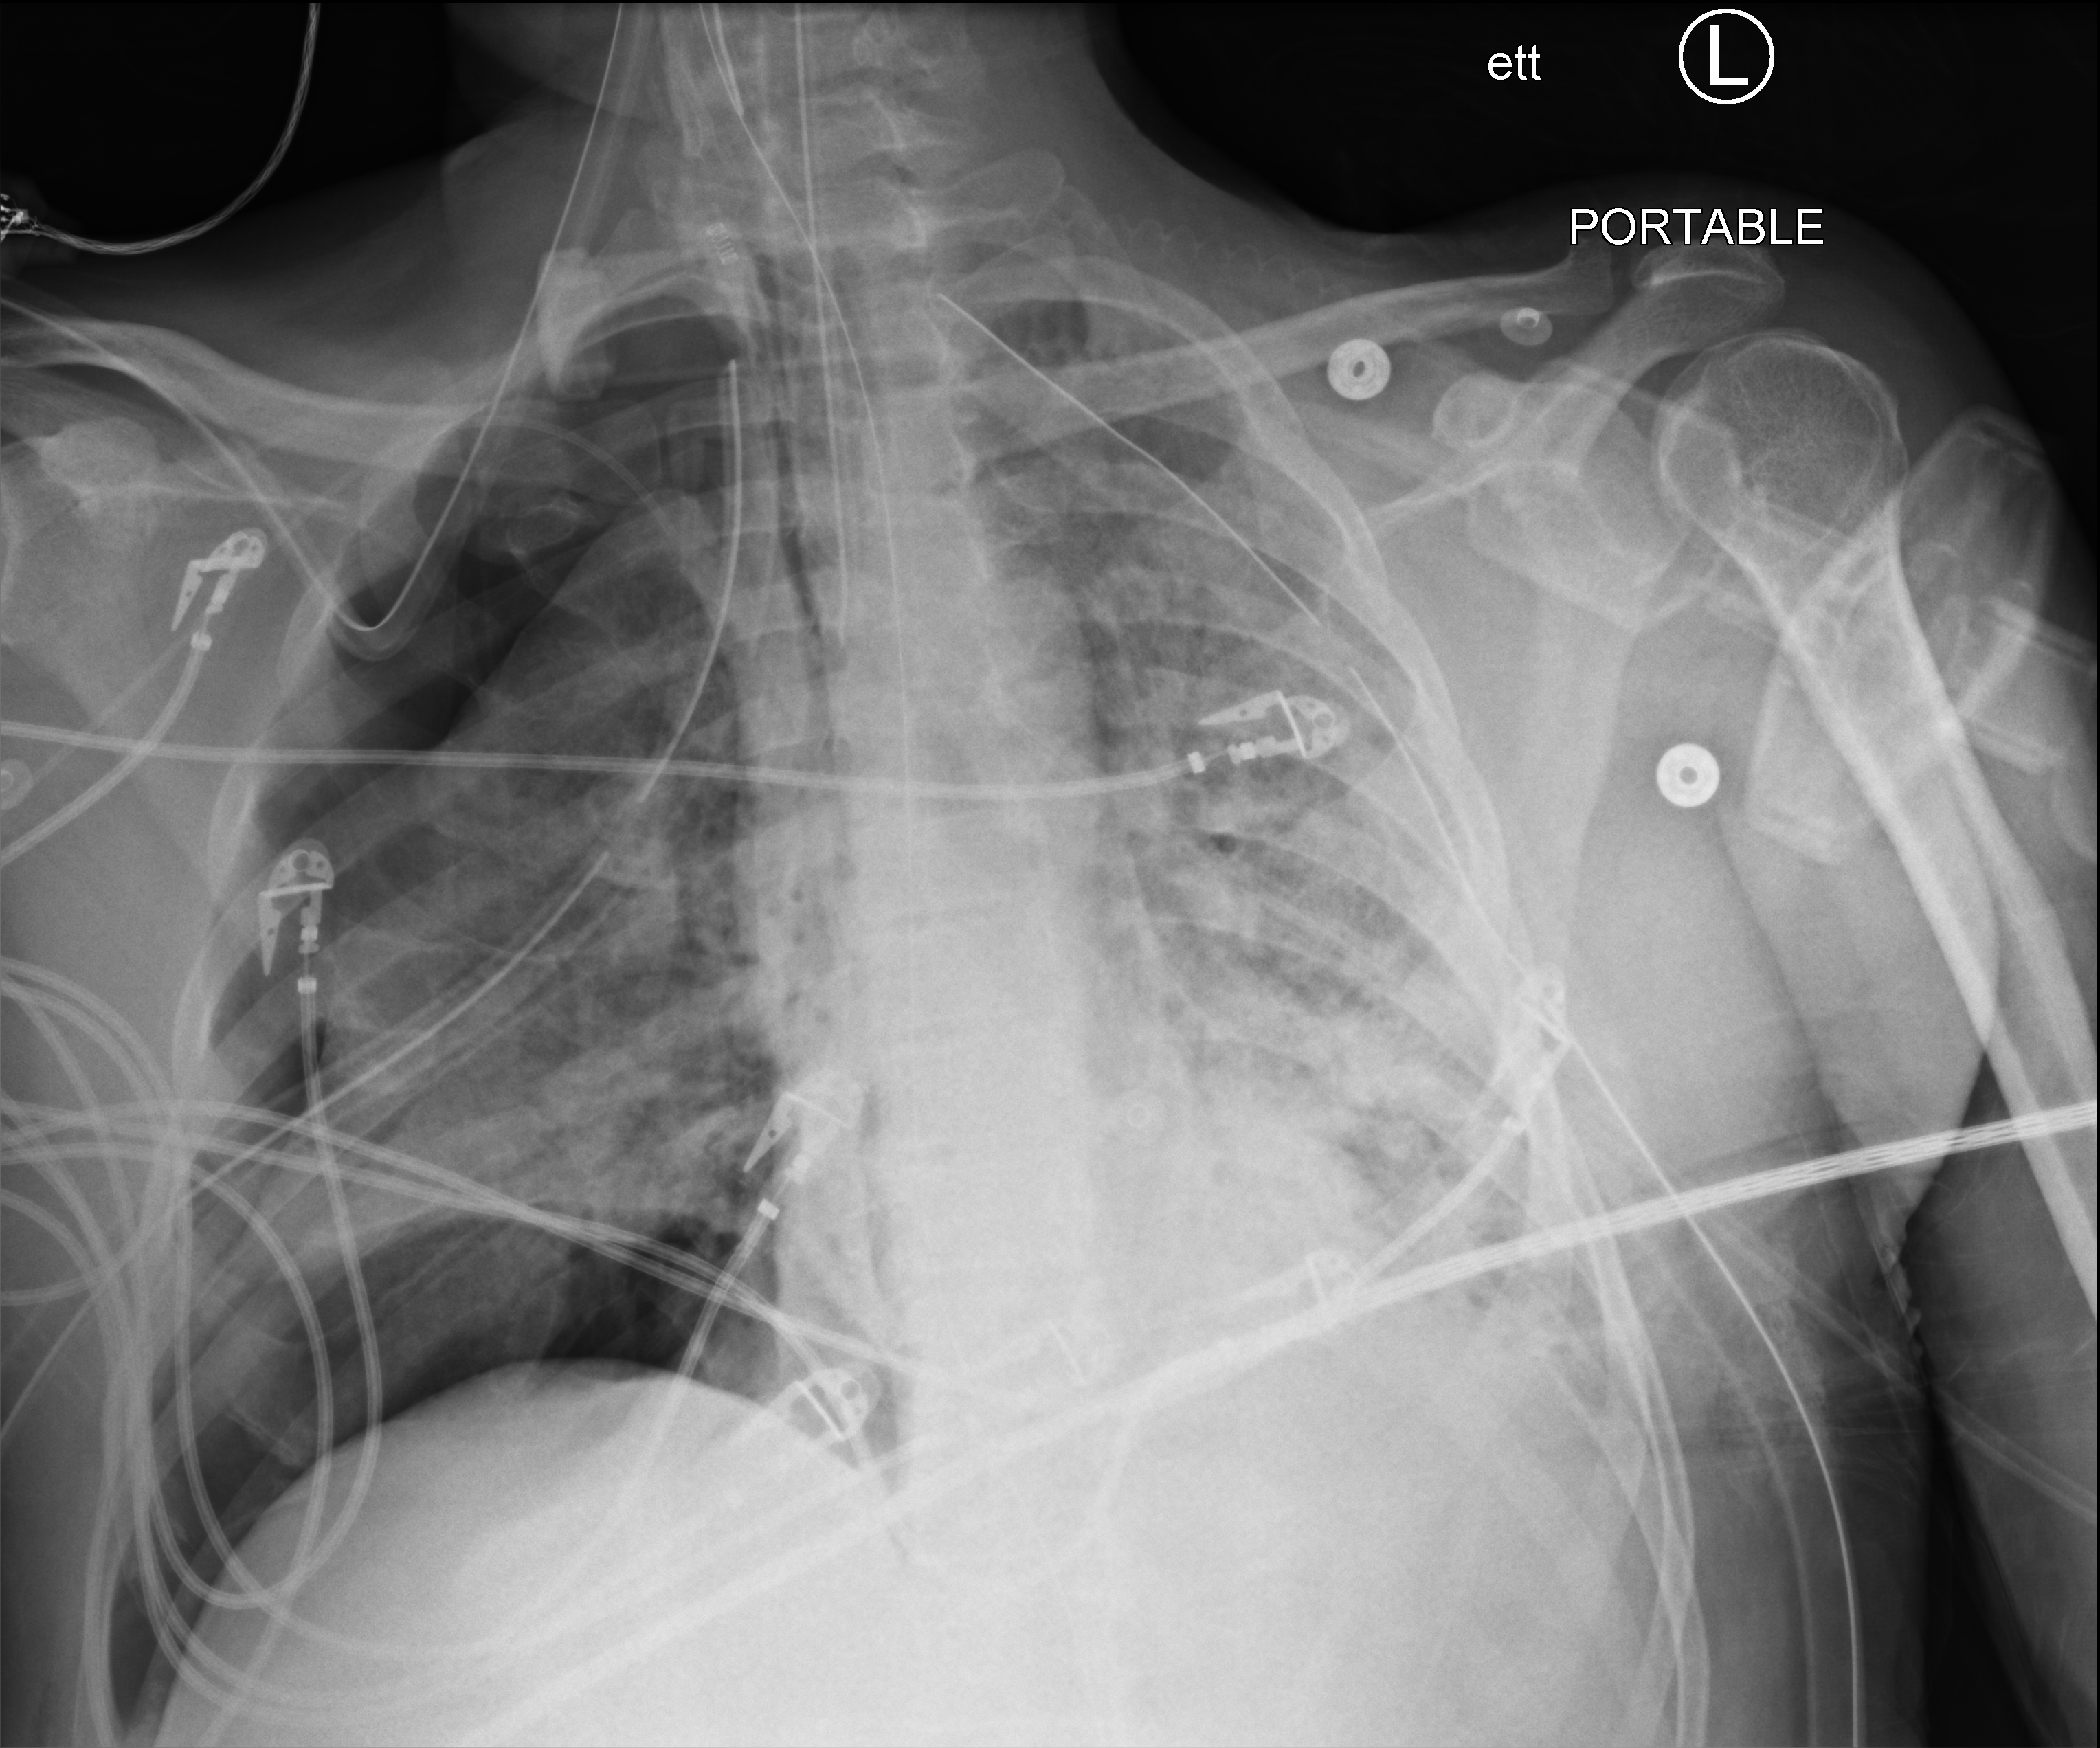
Portable chest radiograph. Male patient hospitalised with COVID-19, age 18–59 years.
Hospital-stay facts (about this admission, not read from this image; timing relative to this image not recorded):
- length of hospital stay: 83 days
- mechanically ventilated during this hospital stay: yes
- admitted to intensive care during this hospital stay: yes